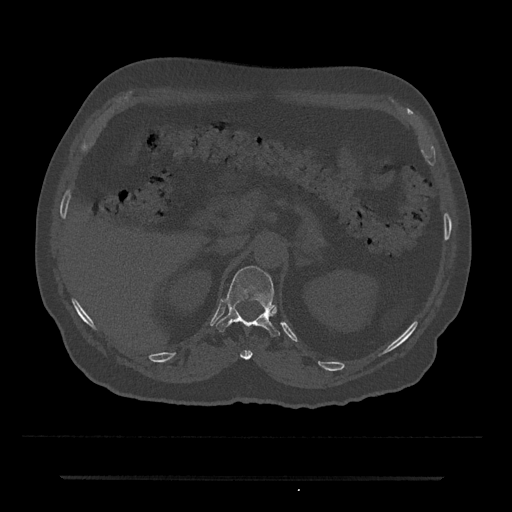
CT including the spine, one axial slice. Position 135 of 797 along the scan axis. Bone window (W 1800 / L 400 HU). 0.5 mm slice thickness. 512 × 512 image matrix, field of view 437 × 437 mm. Patient: male, 69 years. Case-level facts recorded for this patient, not image findings: primary cancer: prostate.
Structures marked on this image (semi-automatically segmented with operator editing):
- T11 vertebra: bounding box [x1, y1, x2, y2] px = [240, 350, 252, 360]
- T12 vertebra: [216, 266, 280, 337]